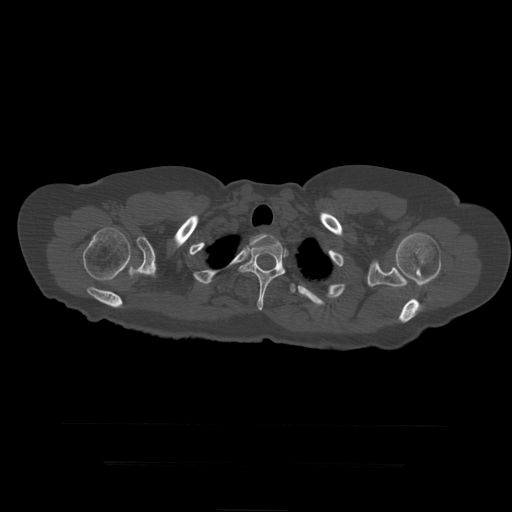
CT including the spine, one axial slice. Slice 364 of 399 in the series (ordered by position). Reconstruction kernel STANDARD. 120 kVp. Bone window (W 1800 / L 400 HU). 1.25 mm slice thickness. 512 × 512 image matrix, field of view 450 × 450 mm. Patient age 41 years. Case-level facts recorded for this patient, not image findings: primary cancer: breast.
Annotated regions visible in this slice (semi-automatic segmentation, software-assisted and operator-edited):
- T2 vertebra: bounding box (x1, y1, x2, y2) in pixels: (250, 234, 283, 247)
- T3 vertebra: (238, 239, 286, 311)
- T4 vertebra: (291, 284, 296, 293)